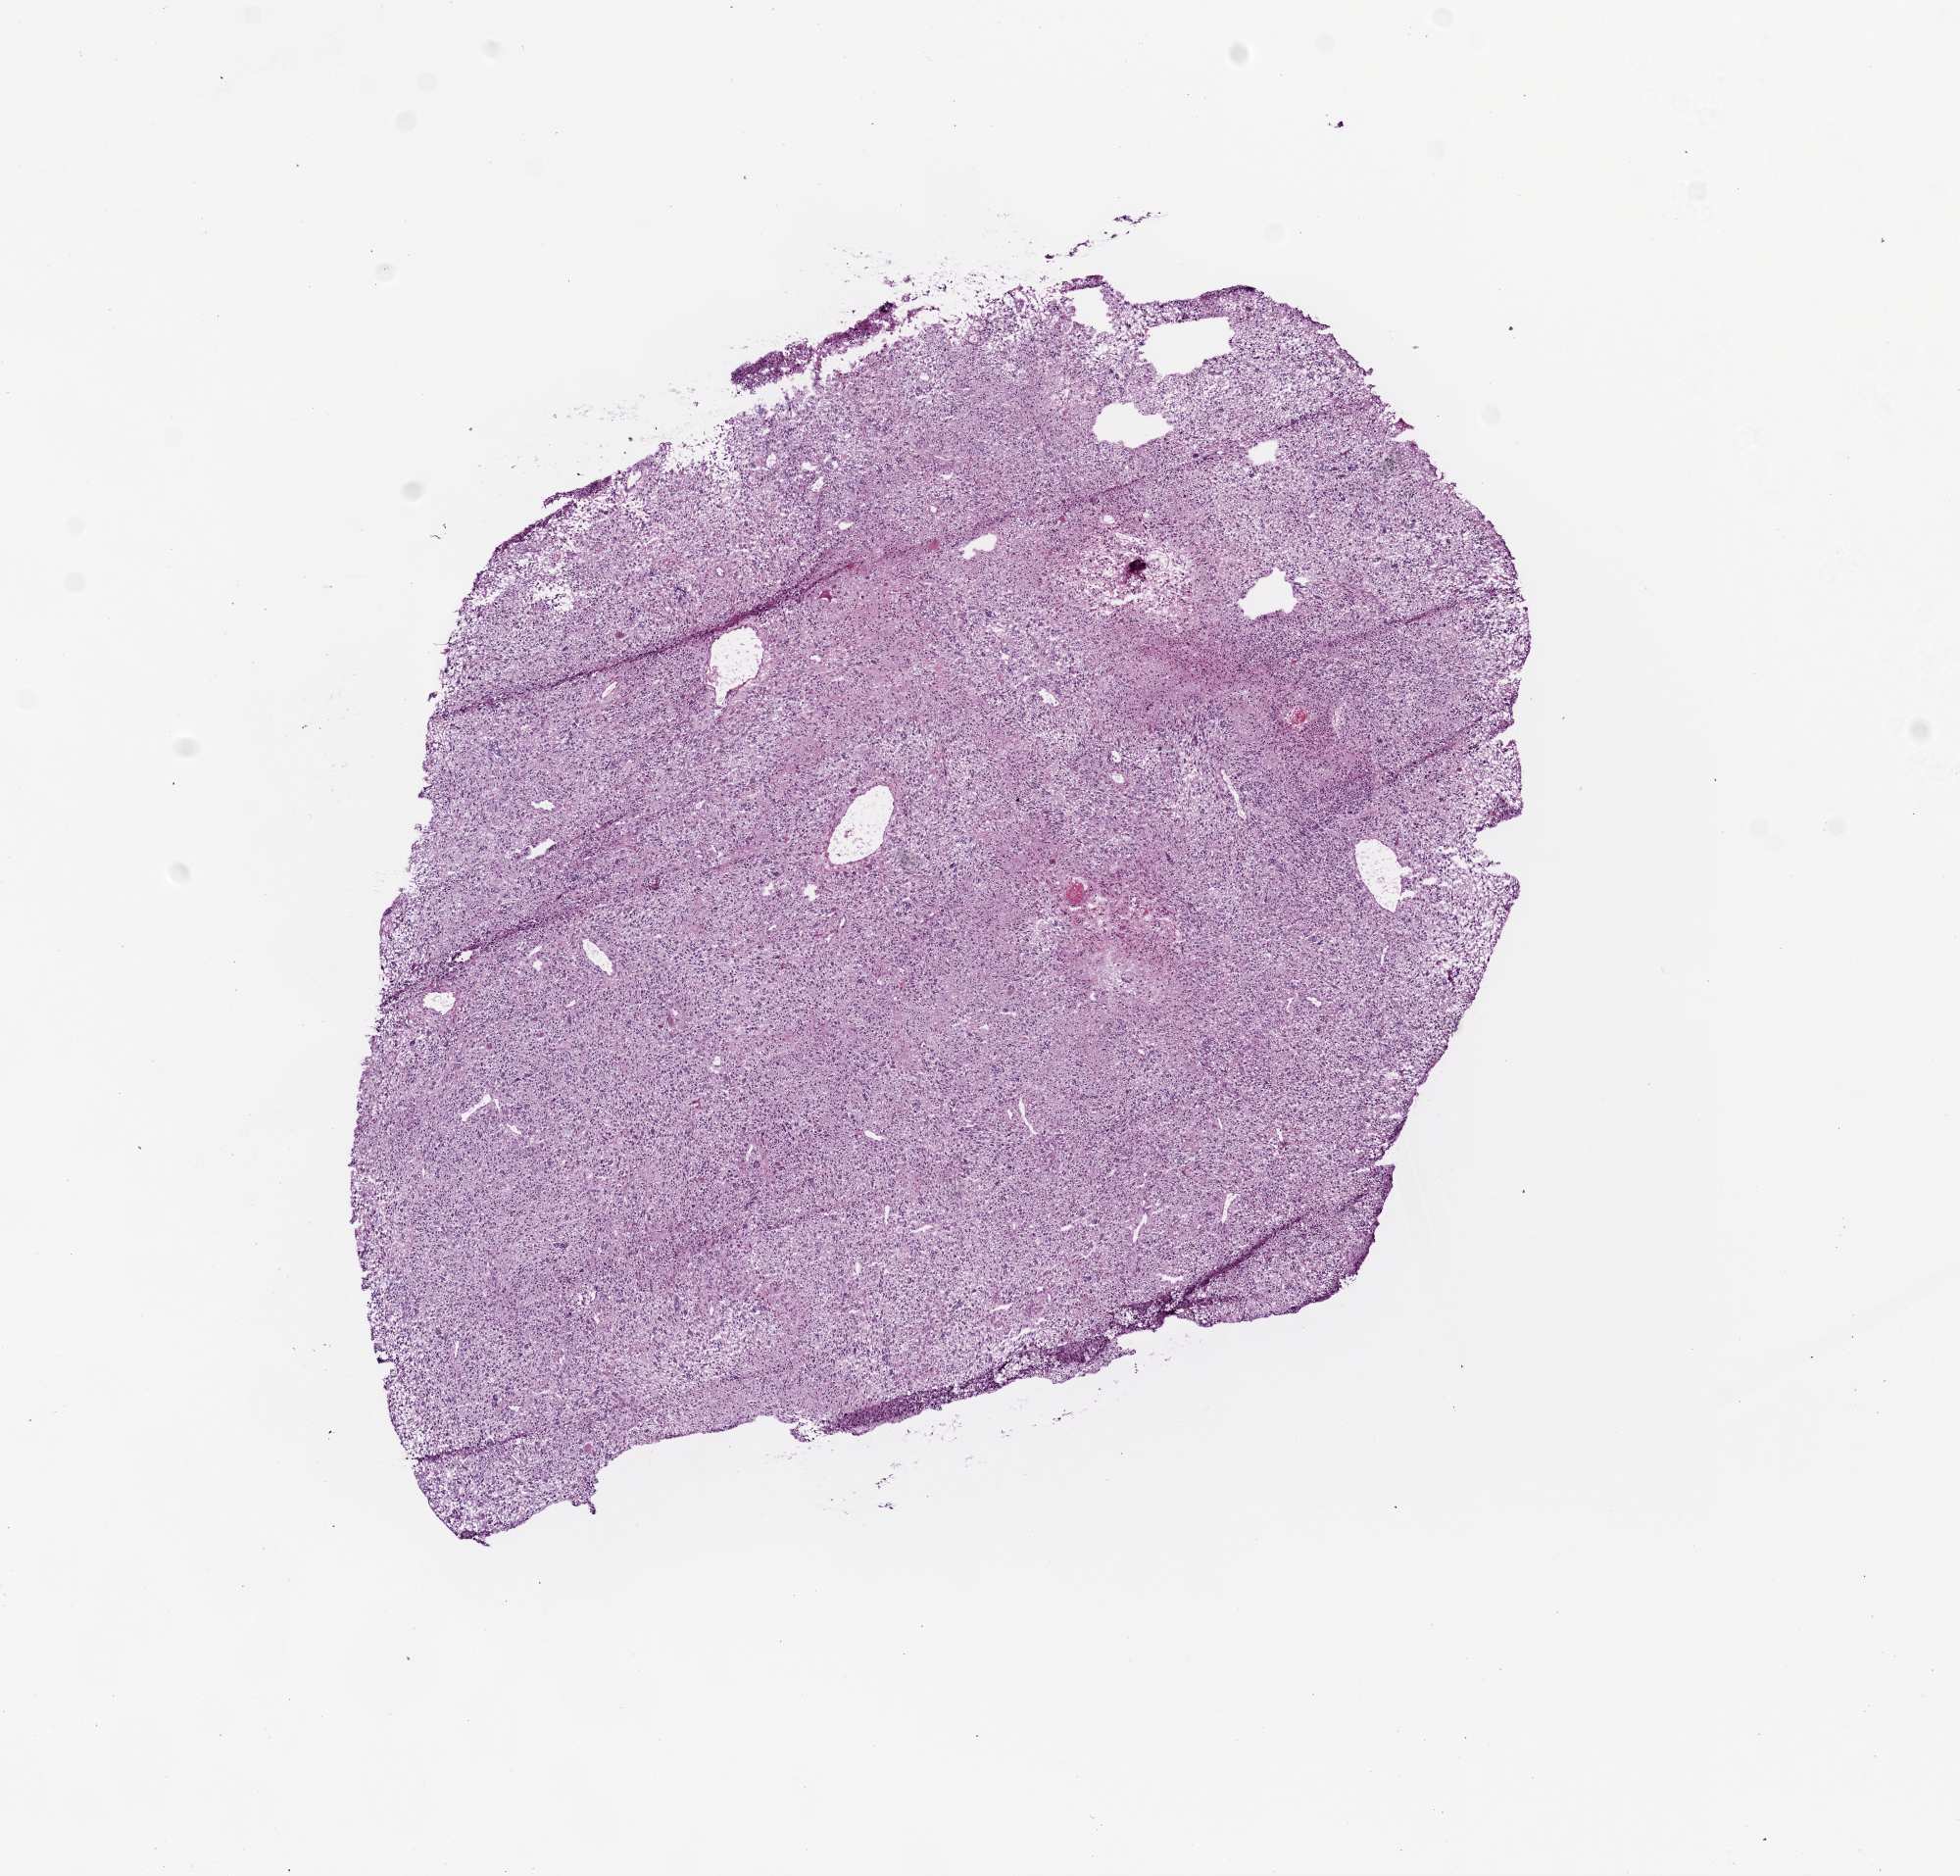
H&E whole-slide image, whole scanned area (about 8.0 x 7.7 mm, acquisition: 20x scan) shown as a low-resolution overview. Frozen section from the top of the tissue portion. Primary tumour sample from the brain. Female patient; age at initial diagnosis 77 years. Composition of this section per pathologist review: tumour cells 97%, tumour nuclei 80%, normal cells 0%, stromal cells 0%, necrosis 3%.
Histologic diagnosis: Glioblastoma.